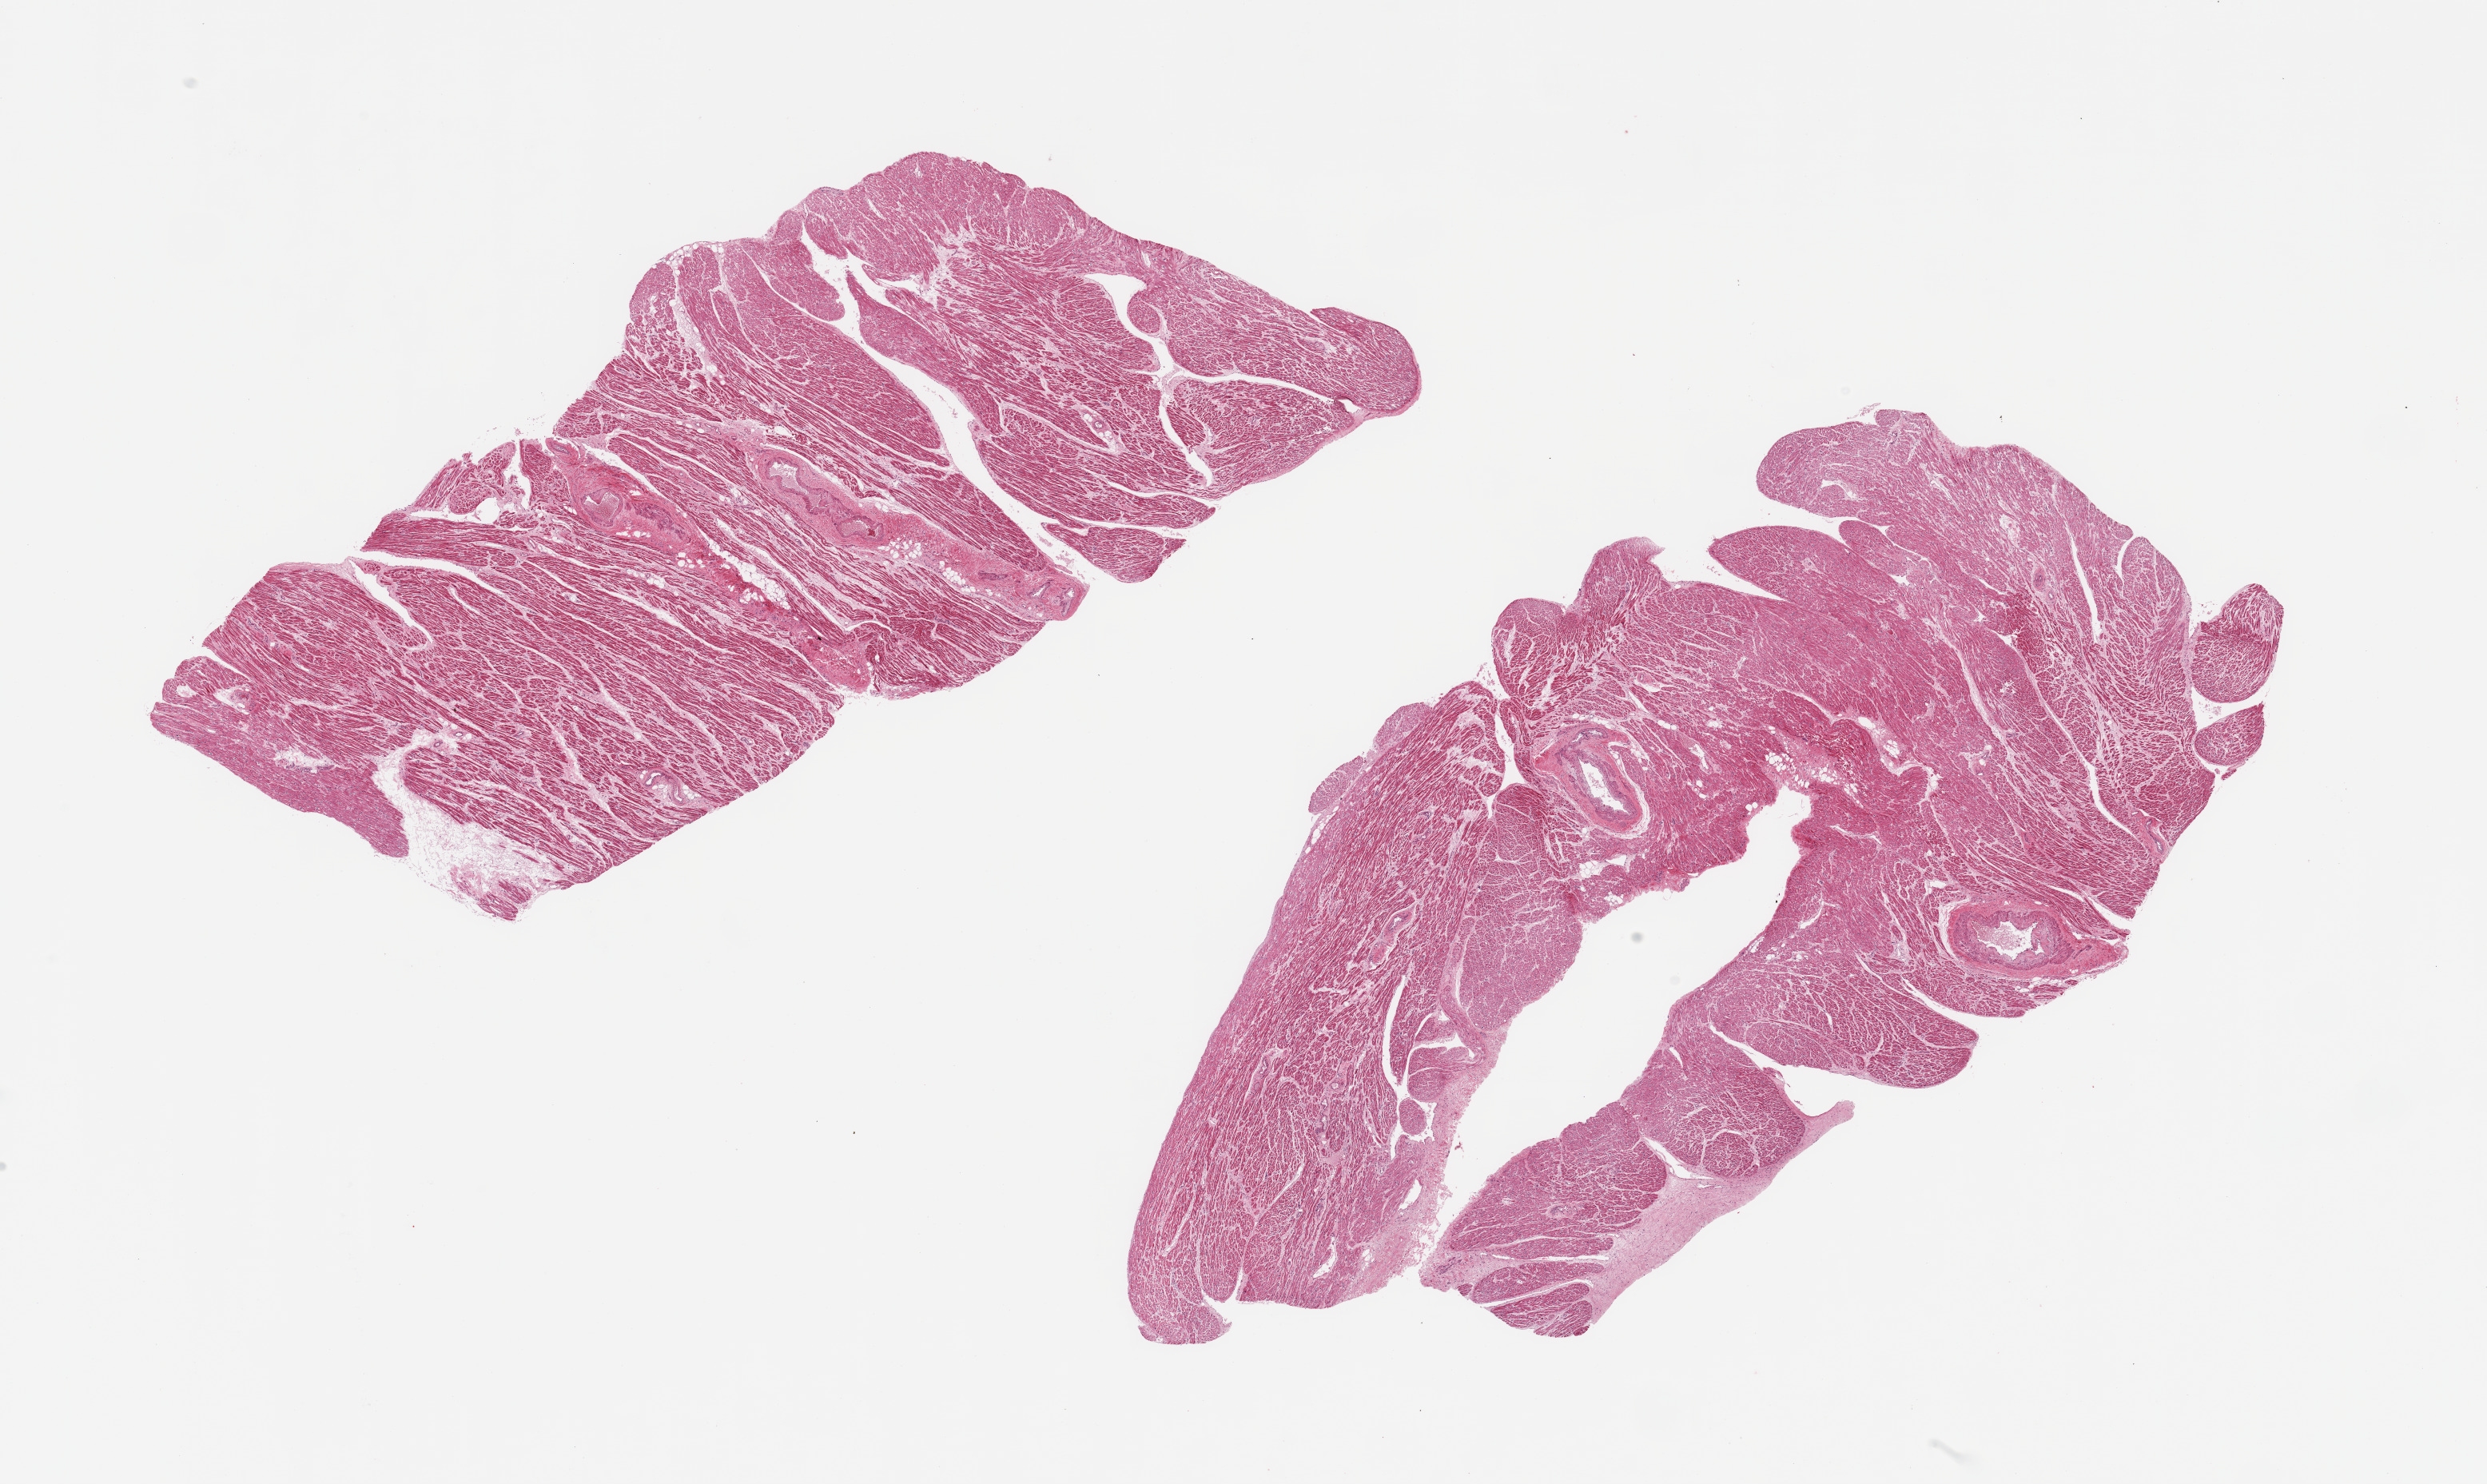
Digitized hematoxylin and eosin (H&E)-stained section, a low-resolution overview of the entire scanned area, about 24.6 x 14.7 mm, PAXgene-fixed paraffin-embedded (PFPE) section, section of auricular appendage (target tissue), tissue donor sample. Donor sex: male.
Review note (as recorded): 2 pieces, no abnormalities.